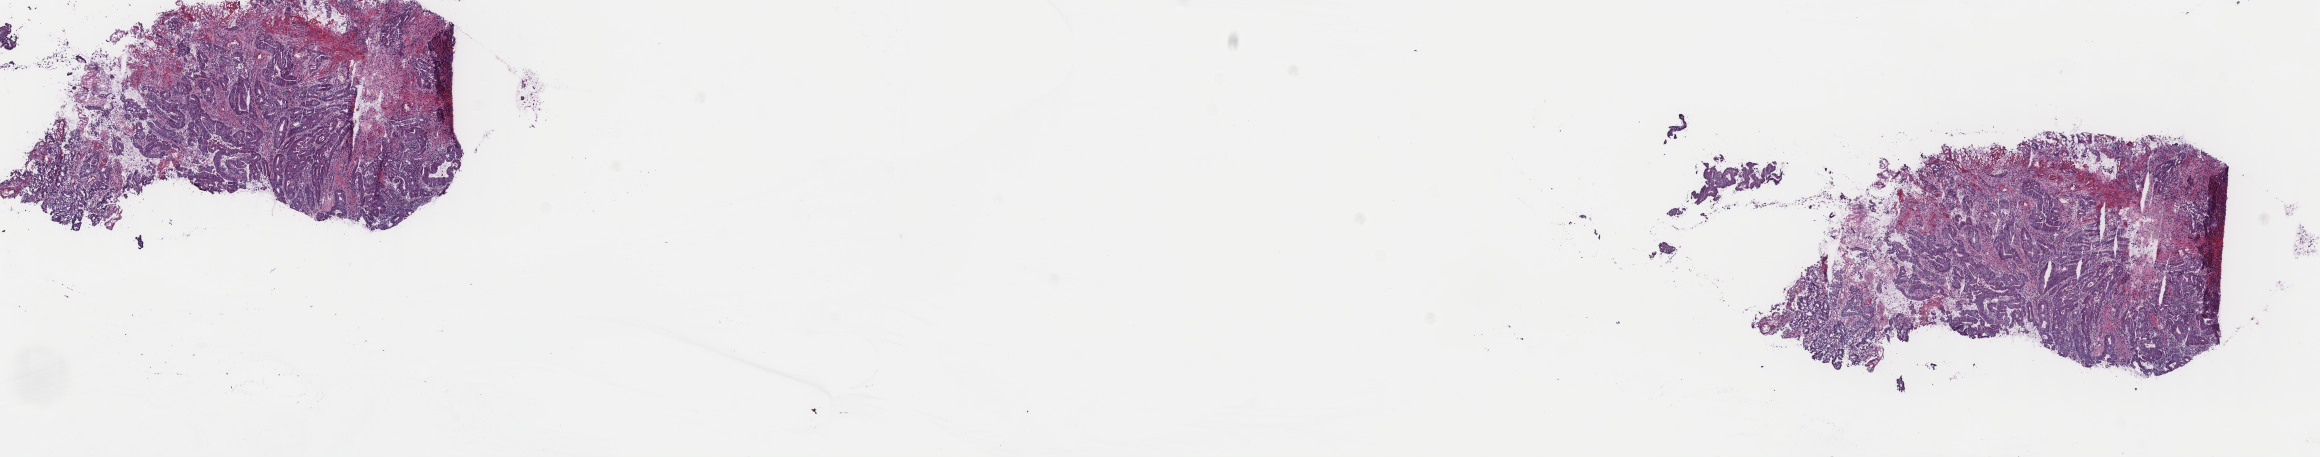
Whole-slide histology image, H&E, low-resolution overview of the scanned area, about 18.4 x 3.6 mm. Frozen section from the top of the tissue portion. Primary tumour sample from the colon. Male, age 69 years at initial diagnosis. Pathologist review of this section (percent, as recorded): tumour cells 70%, tumour nuclei 80%, normal cells 0%, stromal cells 25%, necrosis 5%. Infiltration values recorded for this section: lymphocyte infiltration 0%, monocyte infiltration 0%, neutrophil infiltration 0%.
* diagnosis: Adenocarcinoma, NOS
* lymph nodes positive (case pathology): 4 of 35 examined
* AJCC pathologic stage: IIIB (7th edition)